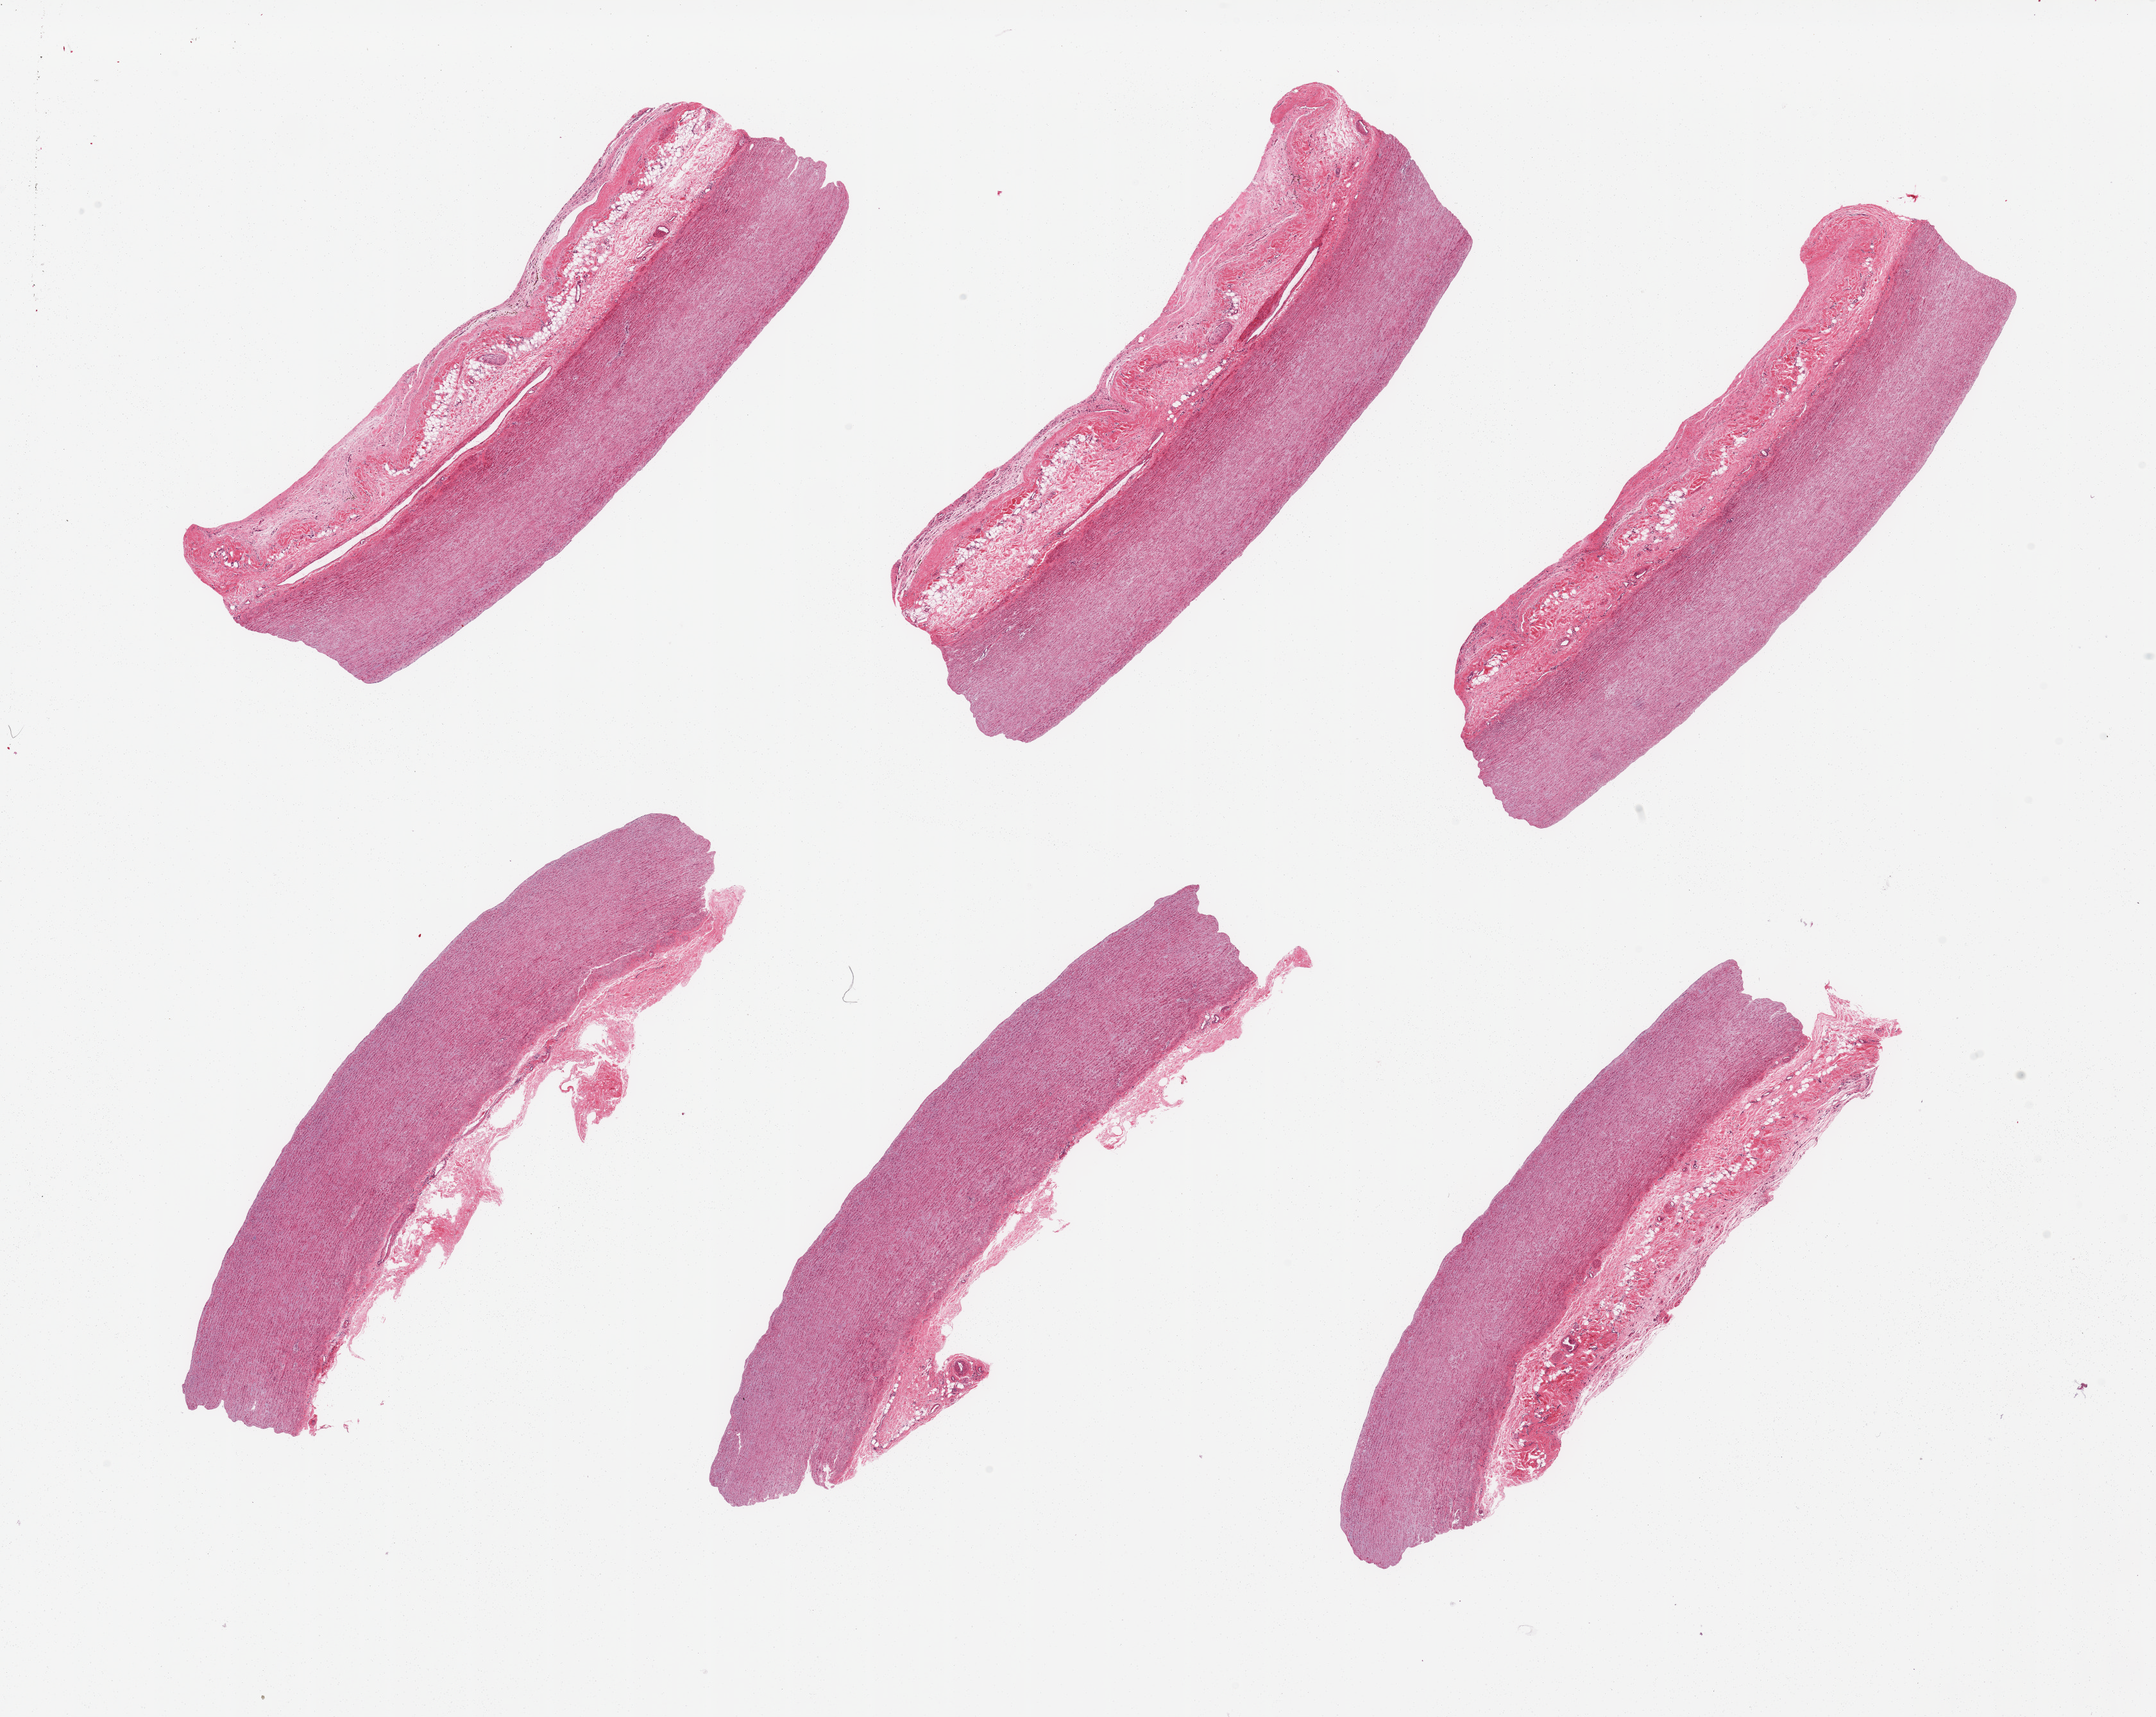
Whole-slide image, hematoxylin and eosin (H&E) stain, brightfield — shown as a low-resolution overview of the whole scanned area (about 26.6 x 21.2 mm); PAXgene-fixed paraffin-embedded (PFPE) section; sampled site (target tissue): aorta; donor tissue sample. Donor sex: male.
* reviewer comment on this tissue sample: 6 pieces; no plaques; several have prominent adventitia 1mm thick